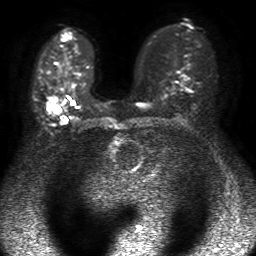
Breast MRI, one axial slice. Slice 30 of 50 in the series (ordered by position). Diffusion-weighted series; image 2 of 4 stored at this slice position (different b-values; order by instance number). 1.5 T. 4 mm slice thickness. 256 × 256 image matrix, field of view 320 × 320 mm. Female patient.
Outlined on this slice (manually delineated by an expert):
- tumour on diffusion-weighted imaging: bounding box [x1, y1, x2, y2] px = [54, 106, 60, 113]